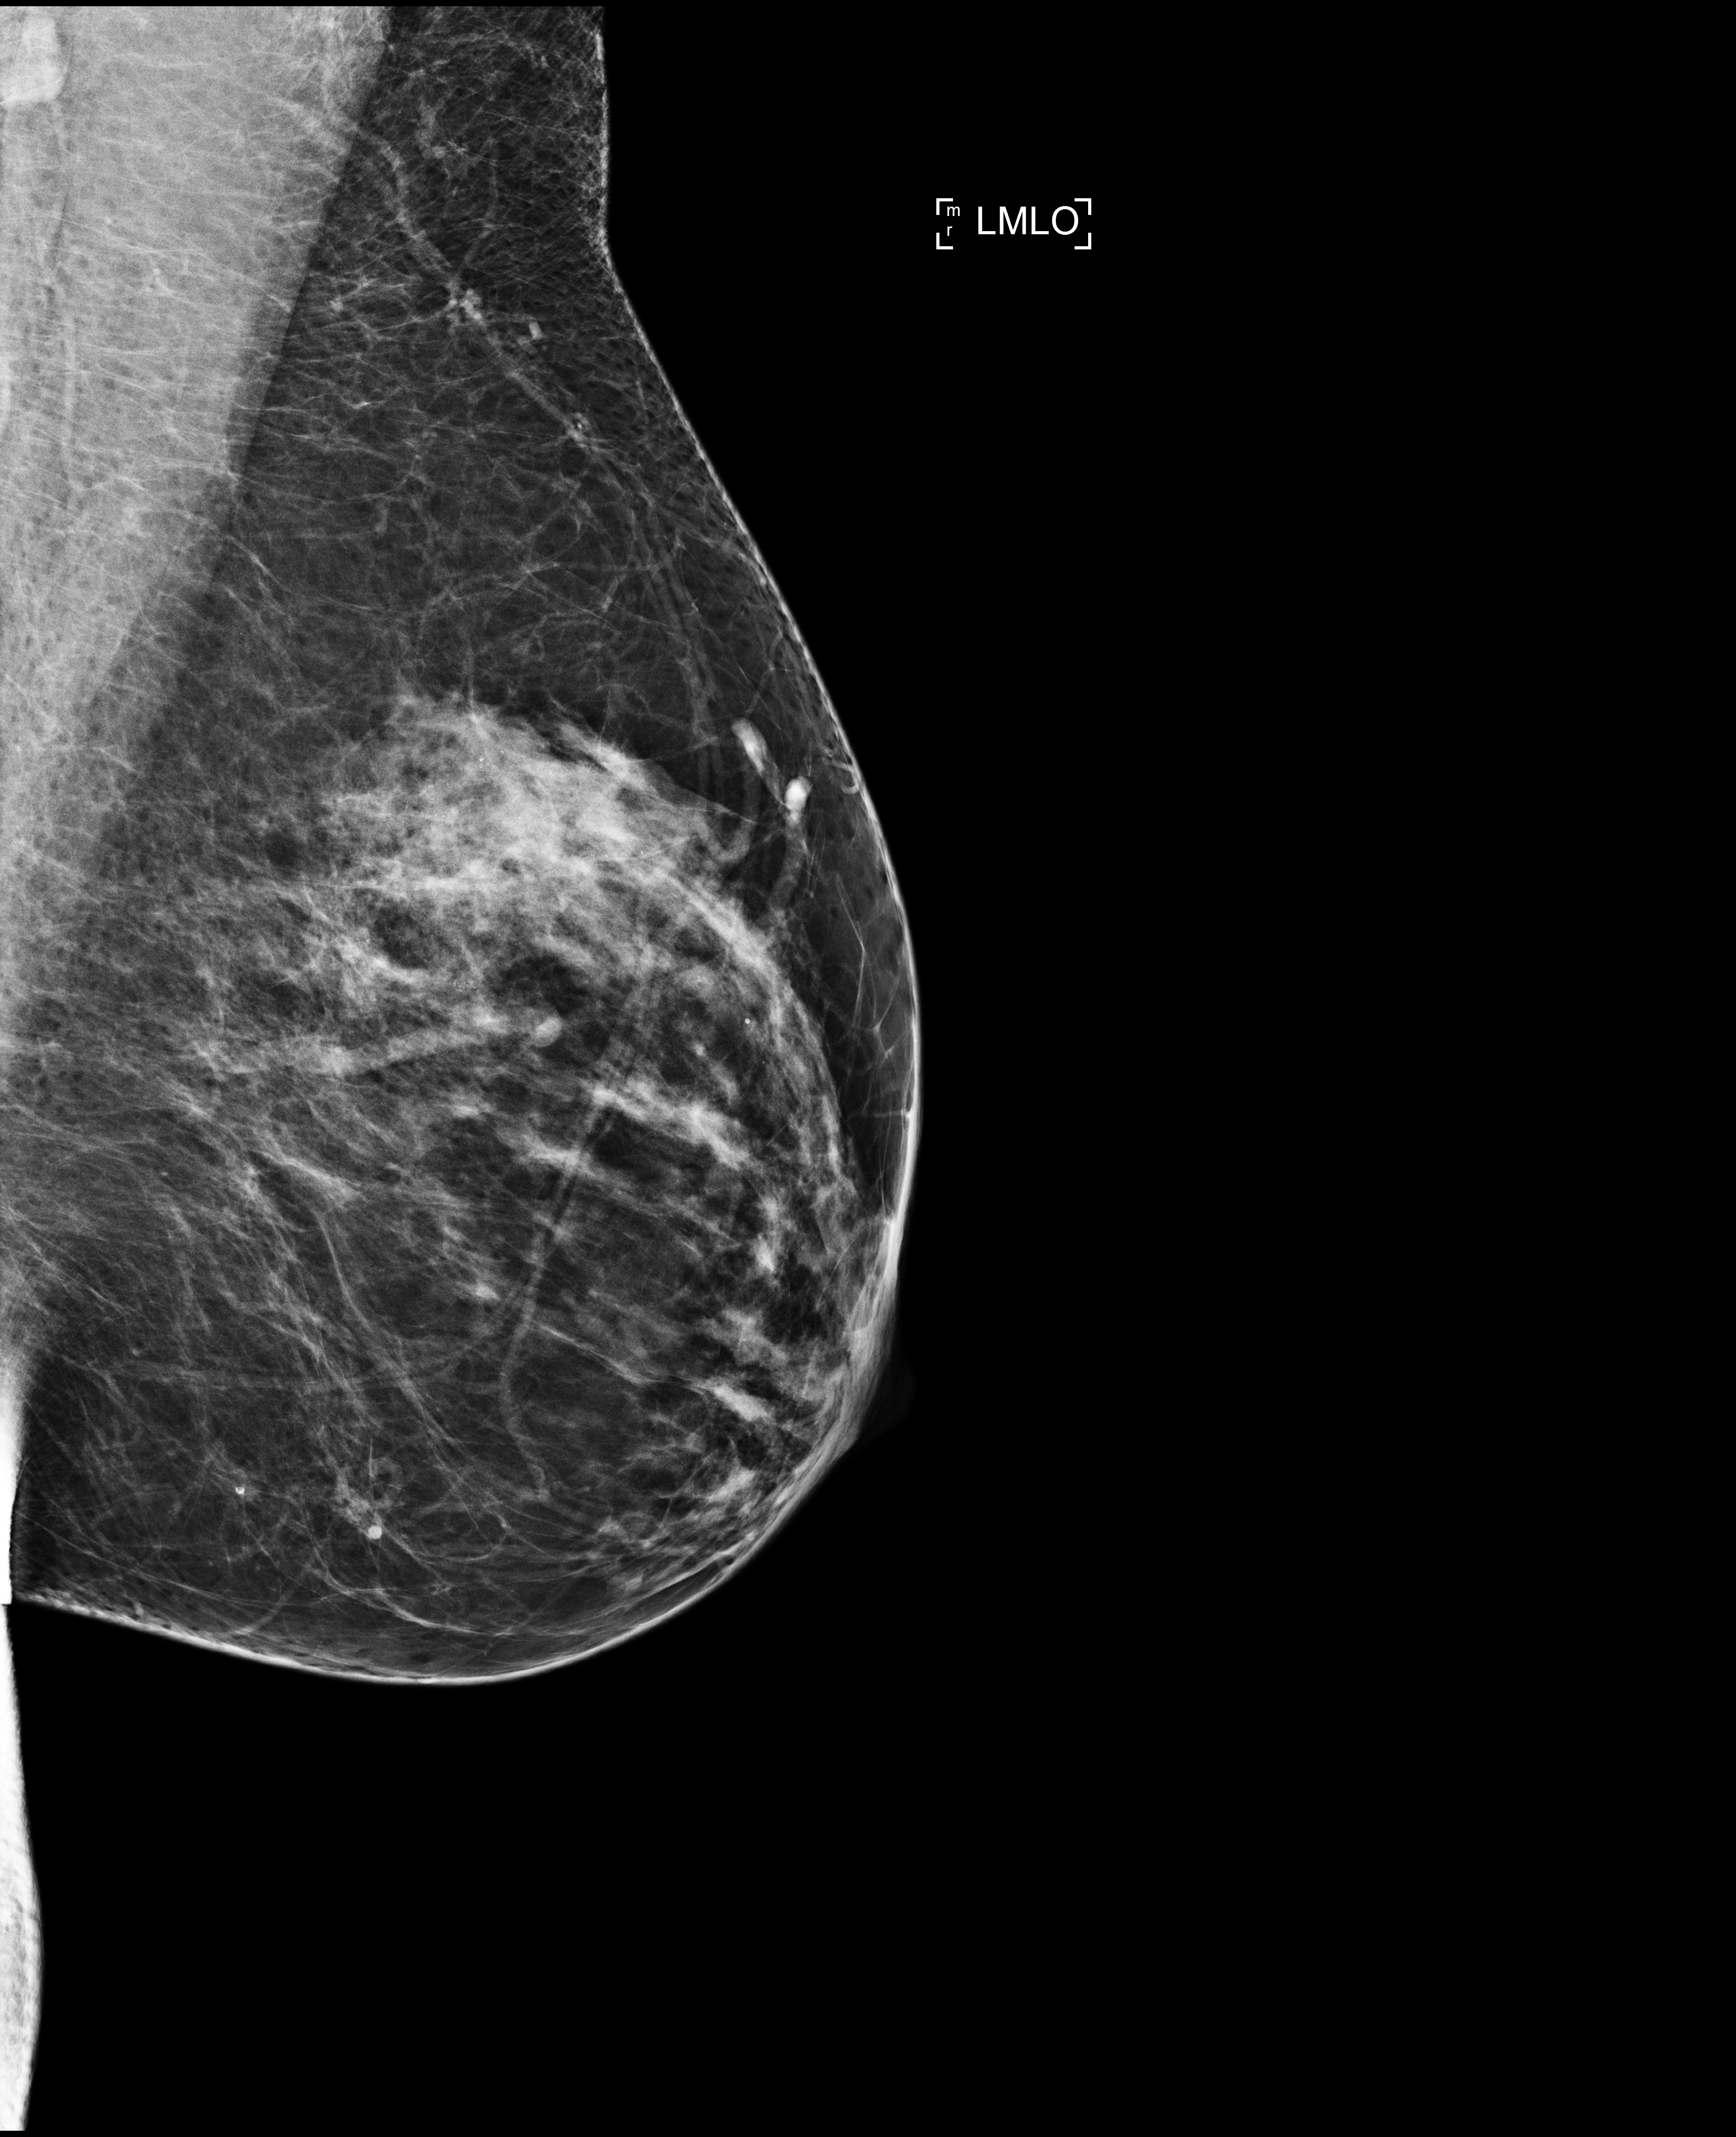
Full-field digital mammogram (FFDM), left breast, MLO view, annual screening mammography examination. Patient aged 59 years (female).
- breast density at the screening exam (both breasts): heterogeneously dense (BI-RADS density category c)
- final BI-RADS assessment for this screening round (tomosynthesis exam, both breasts): category 2
- recall: no recall after this screen